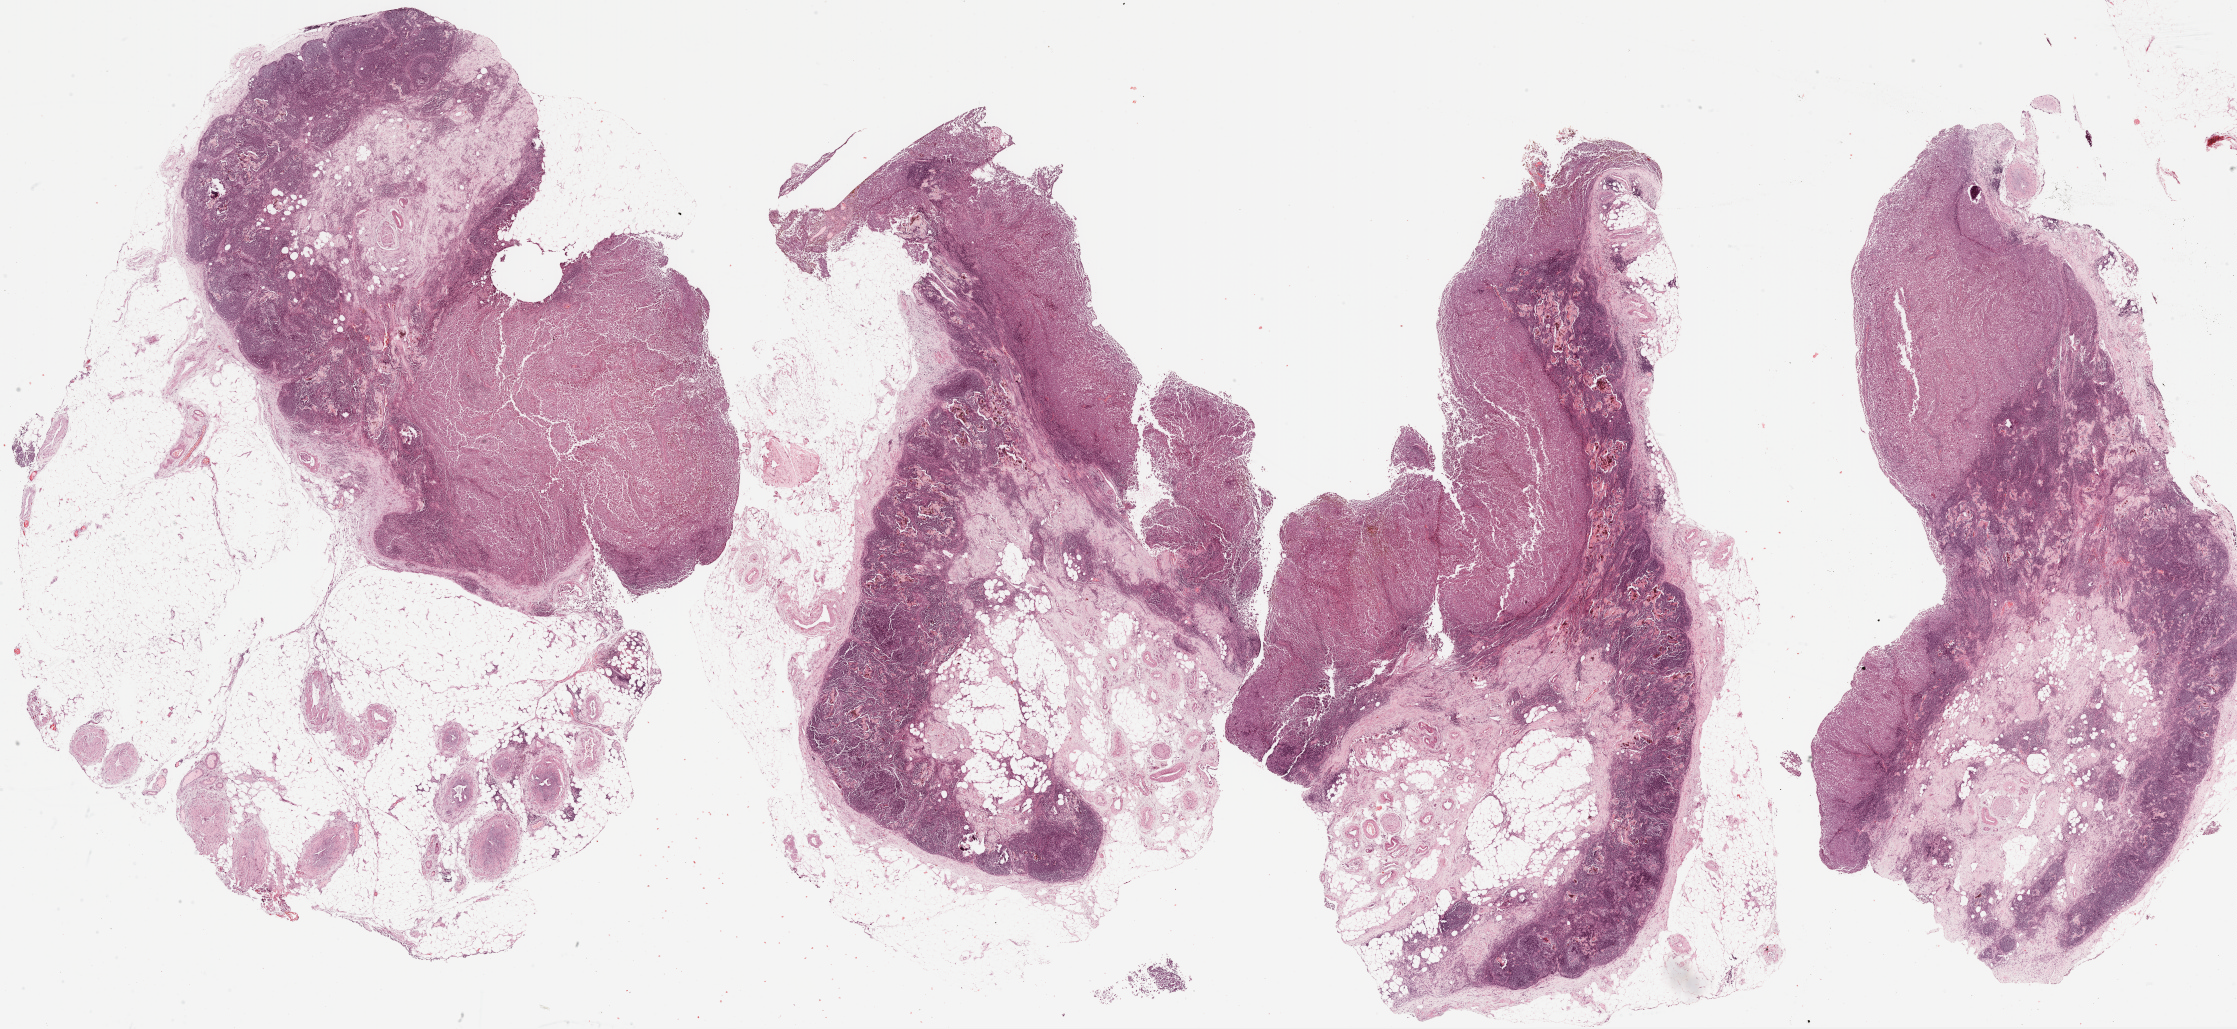
Whole-slide histology image, Hematoxylin and eosin (H&E) stained — whole scanned area (about 36.1 x 16.6 mm) shown as a low-resolution overview. FFPE section. Metastatic tumour sample, sampled site: lymph node. Female patient; age at initial diagnosis 75 years.
This section: metastatic tumour tissue. Patient diagnosis: Malignant melanoma, NOS.